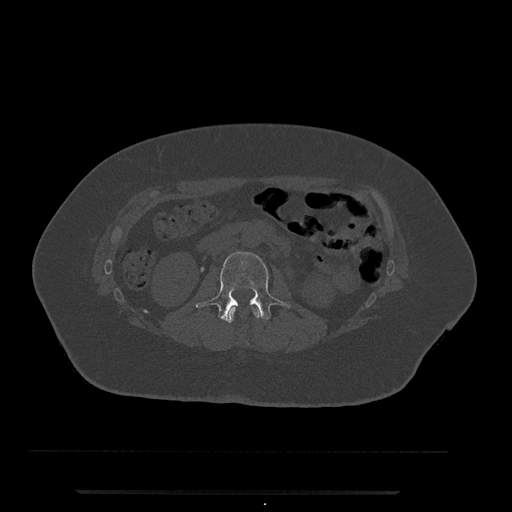
CT including the spine, one axial slice; slice 46 of 797 in the series (ordered by position); reconstruction kernel Br40s/3; 120 kVp; bone window (W 1800 / L 400 HU); 512 × 512 image matrix, field of view 440 × 440 mm. Female patient, age 51 years. From the clinical record (not read from this slice): primary cancer: neuro.
Structures marked on this image (semi-automatically segmented with operator editing):
- L1 vertebra: bounding box [x1, y1, x2, y2] px = [227, 307, 261, 323]
- L2 vertebra: [195, 251, 291, 322]